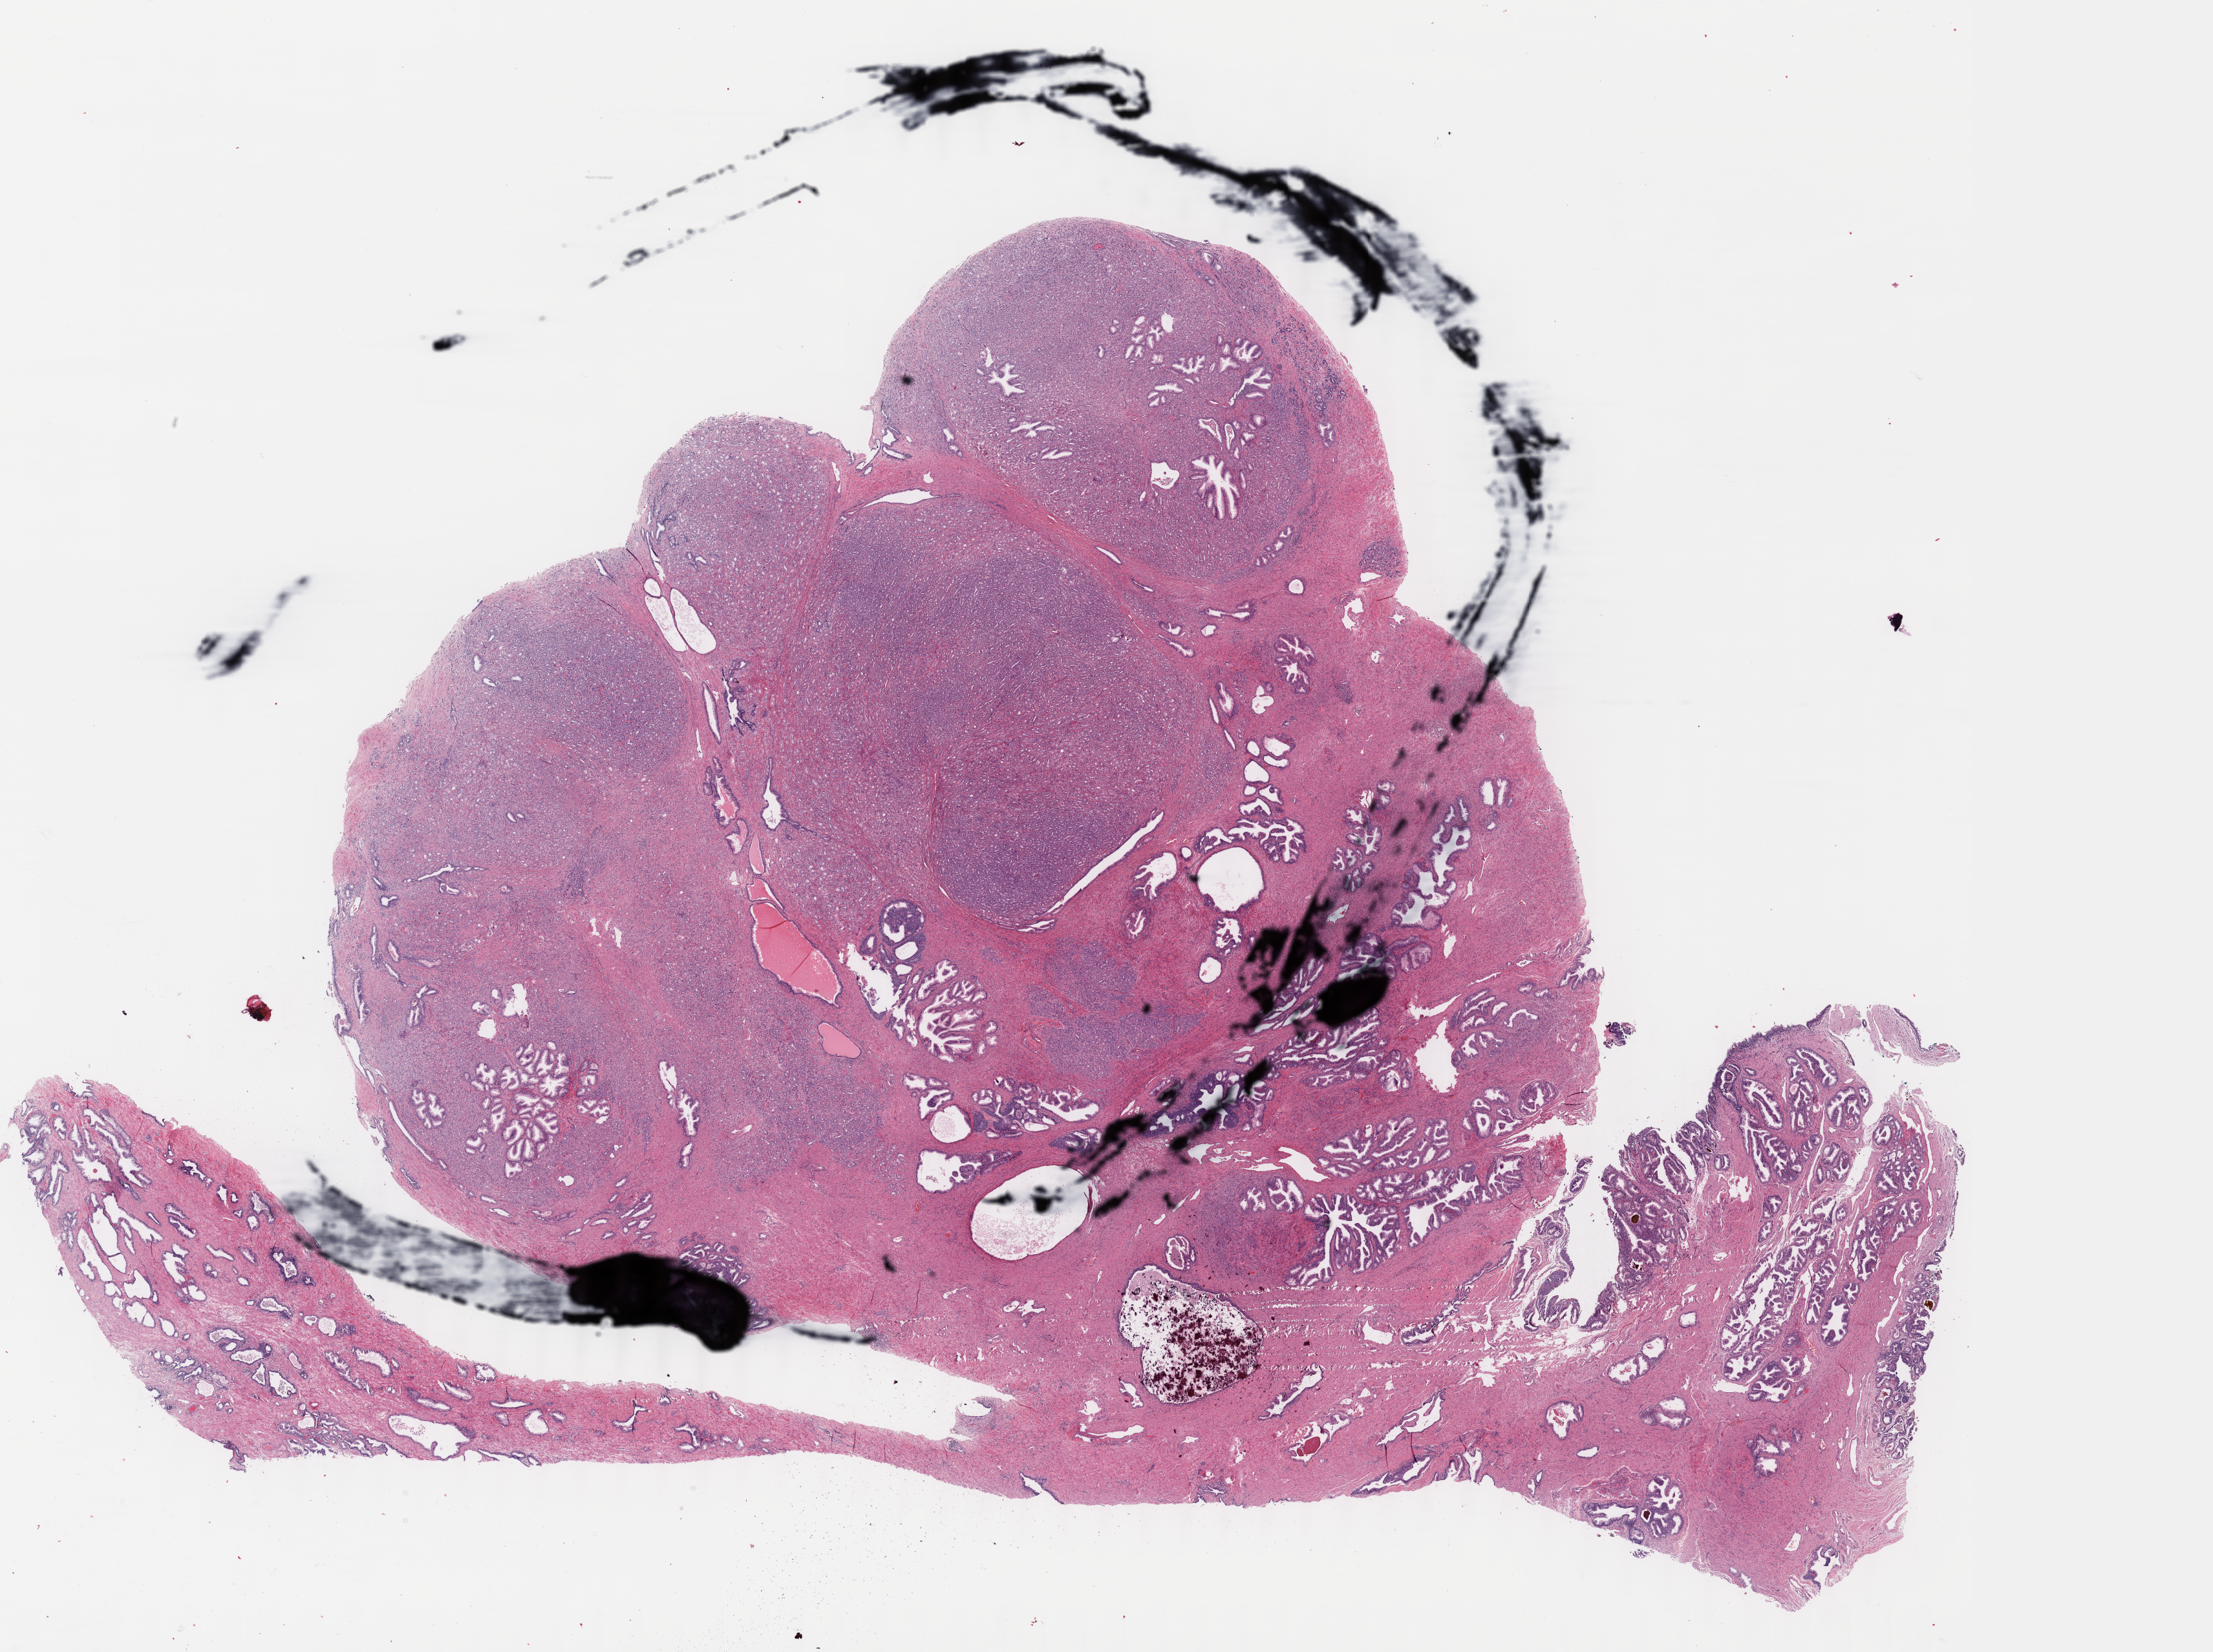
Hematoxylin and eosin (H&E) stained whole-slide image — low-resolution overview of the scanned area, about 27.2 x 20.3 mm. FFPE section. Prostate, primary tumour sample. Patient: male, age at initial diagnosis 58 years. Gleason score: 9 (4+5).
- diagnosis: Adenocarcinoma, NOS (prostate gland)